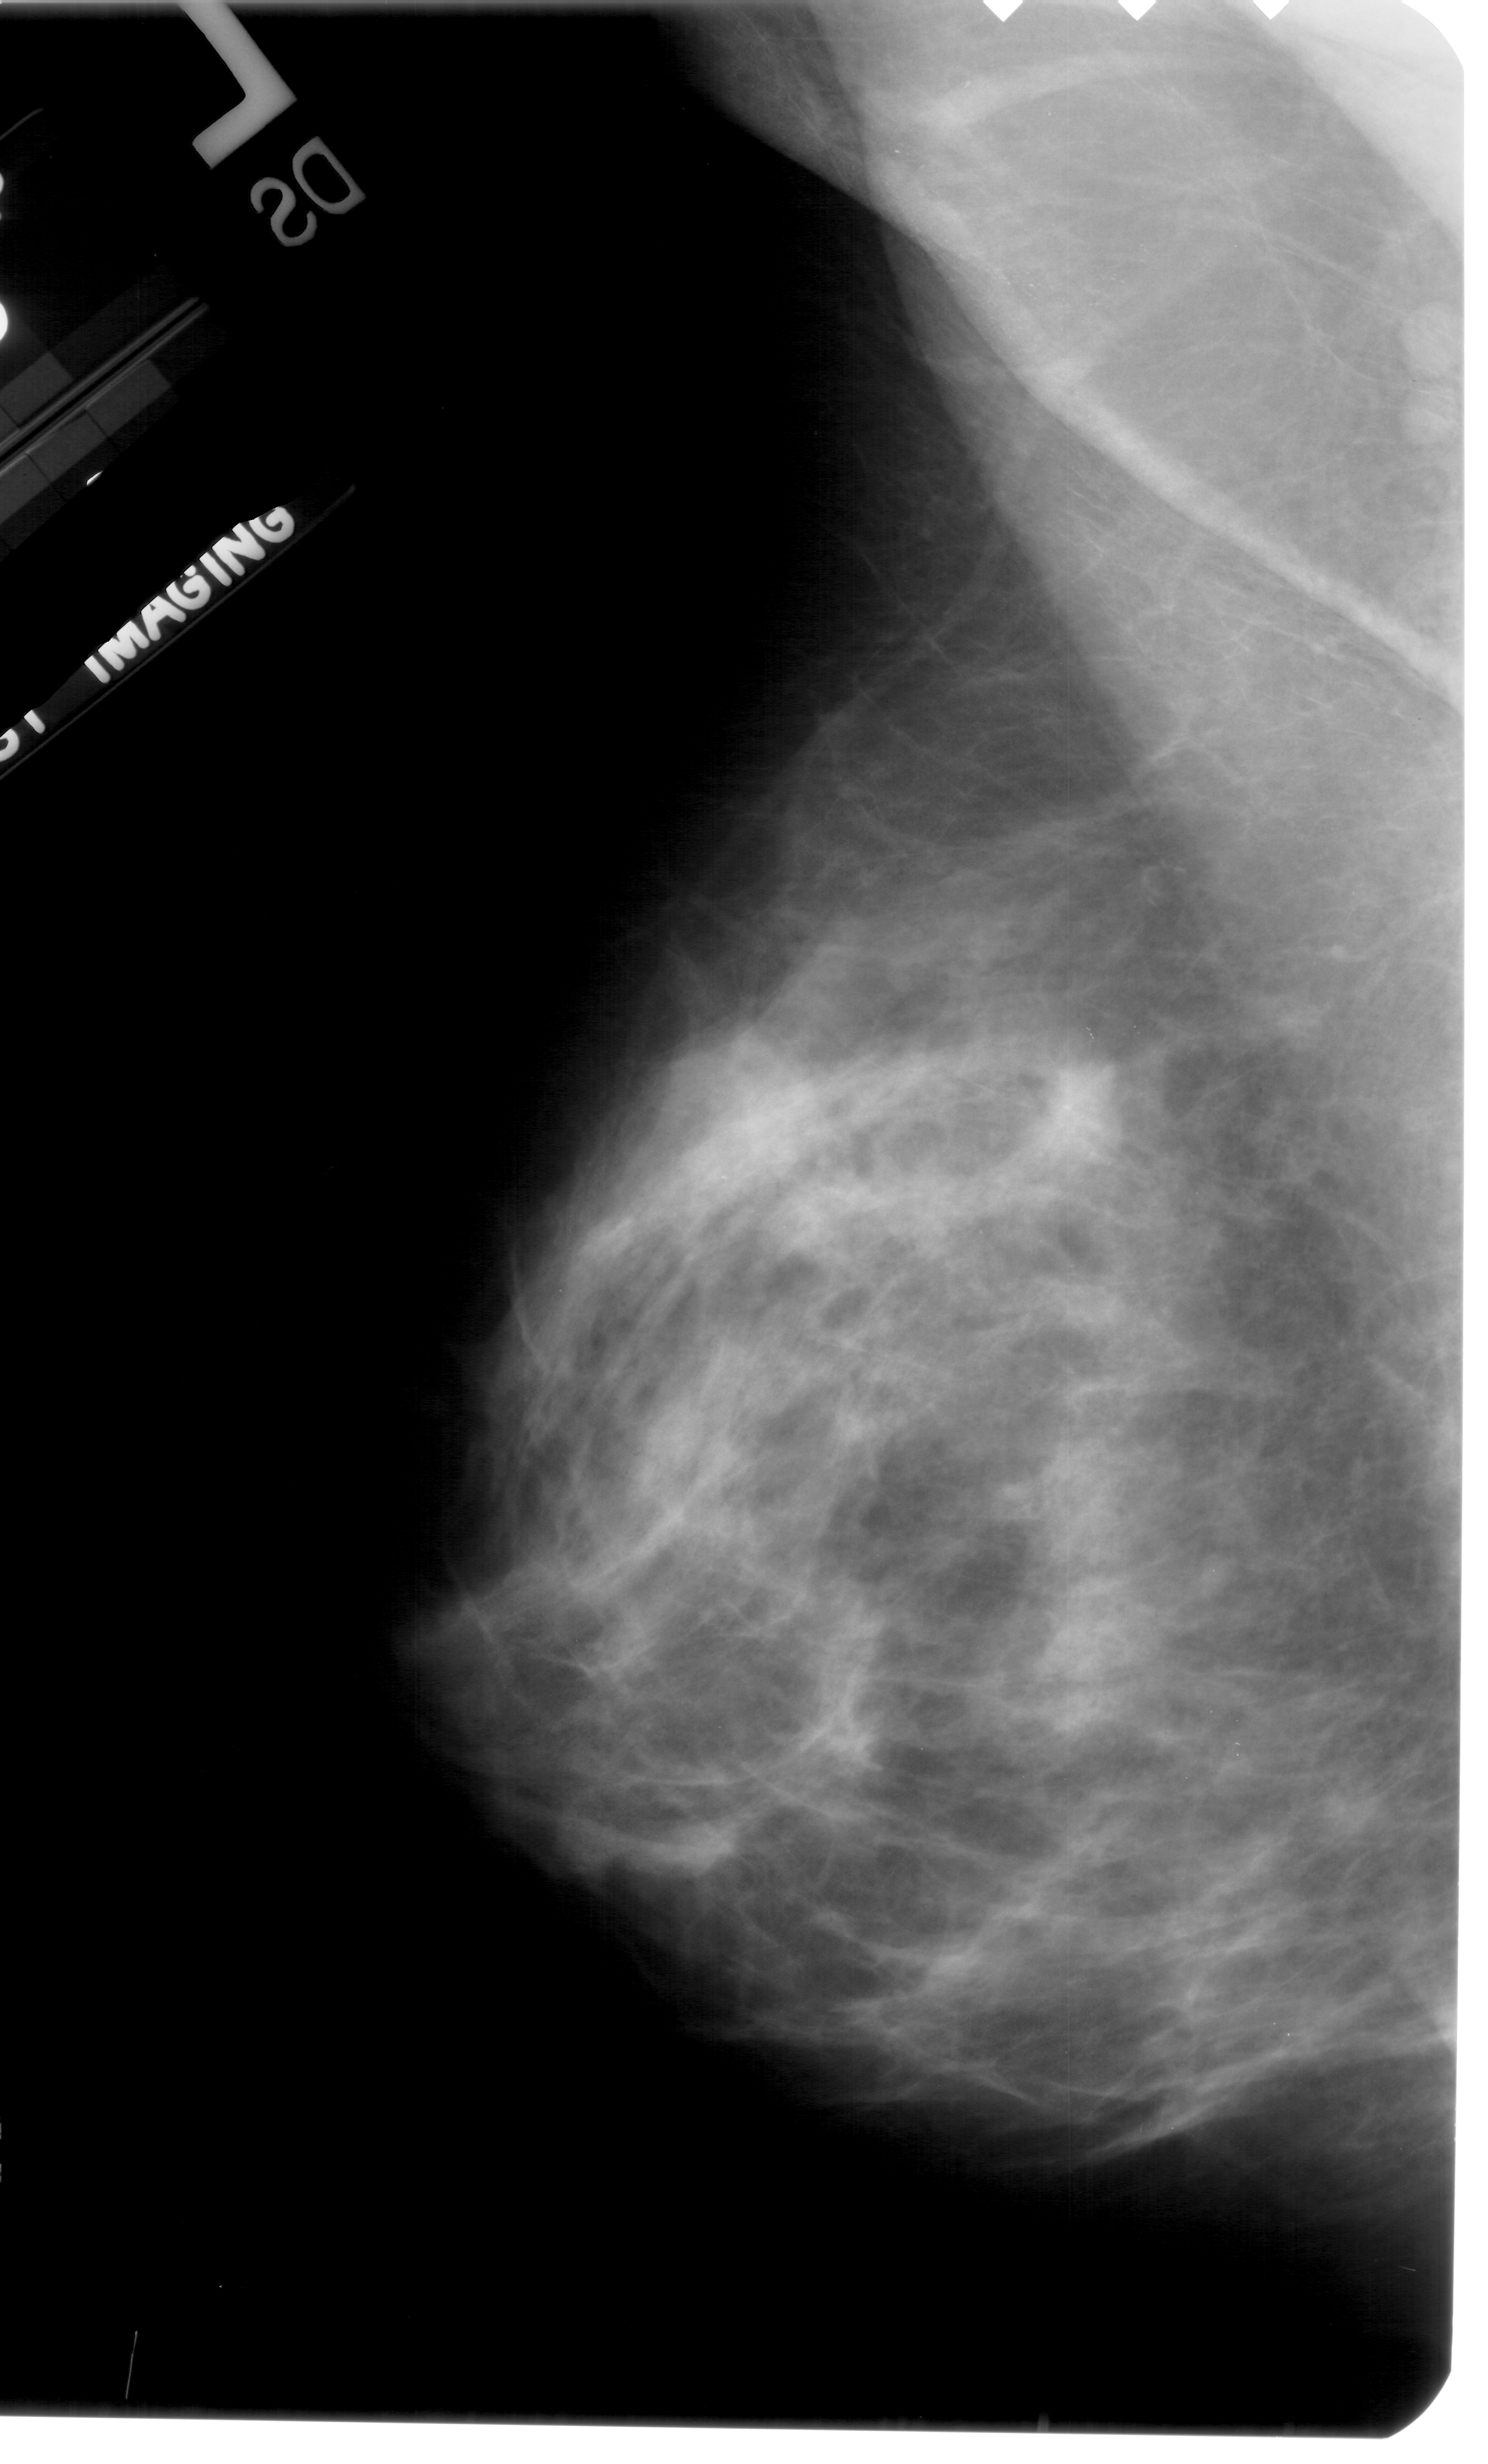
Digitized screen-film mammogram; left breast; mediolateral oblique (MLO) view.
Radiologist-marked abnormalities on this image: mass, shape focal asymmetric density, margins ill defined; BI-RADS assessment category 4; subtlety rating 3 on a 1 (subtle) to 5 (obvious) scale; pathology (as recorded): malignant.